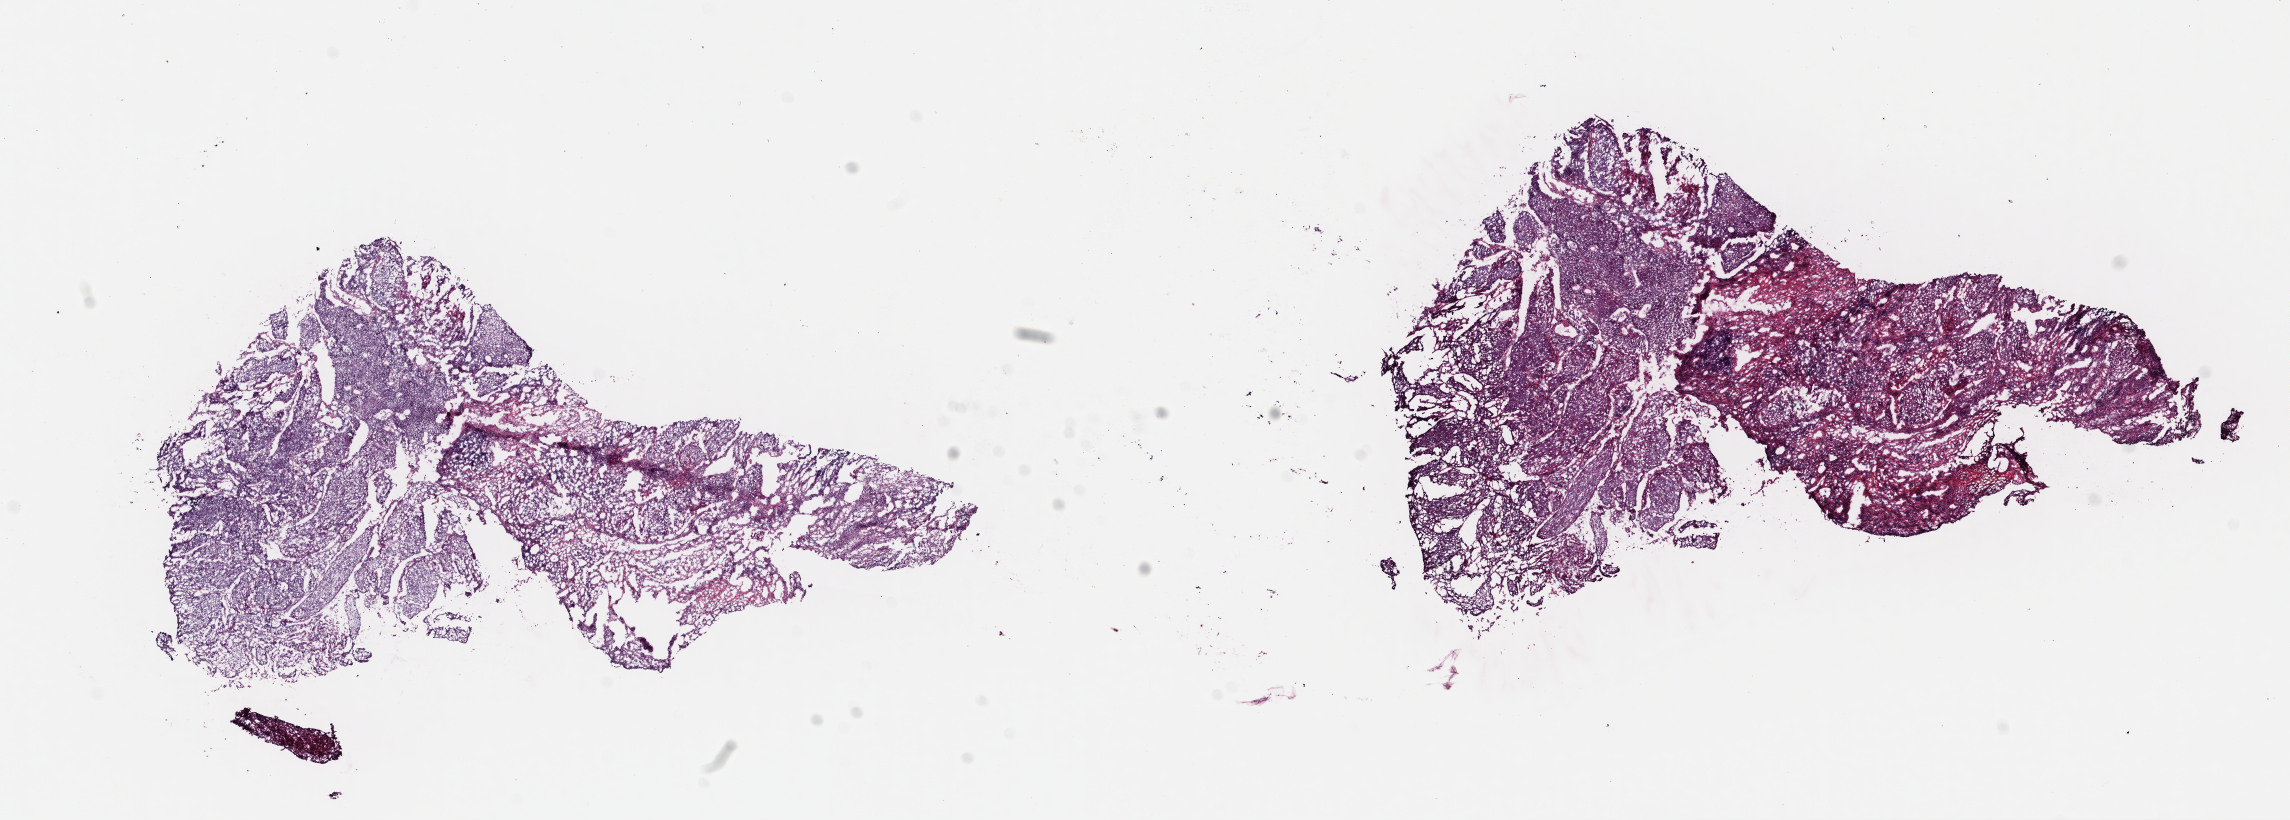
Whole-slide histology image, H&E-stained, low-resolution overview of the scanned area, about 18.0 x 6.4 mm, frozen section from the top of the tissue portion, cervix, primary tumour sample. Female, age 65 years at initial diagnosis. Histologic grade: G2 (moderately differentiated). Pathologist review of this section (percent, as recorded): tumour cells 70%, tumour nuclei 65%, normal cells 0%, stromal cells 30%, necrosis 0%. Inflammatory infiltration, as recorded: lymphocyte infiltration 0%, monocyte infiltration 0%, neutrophil infiltration 0%.
* histologic diagnosis: Squamous cell carcinoma, NOS (cervix uteri)
* FIGO stage: IIIB